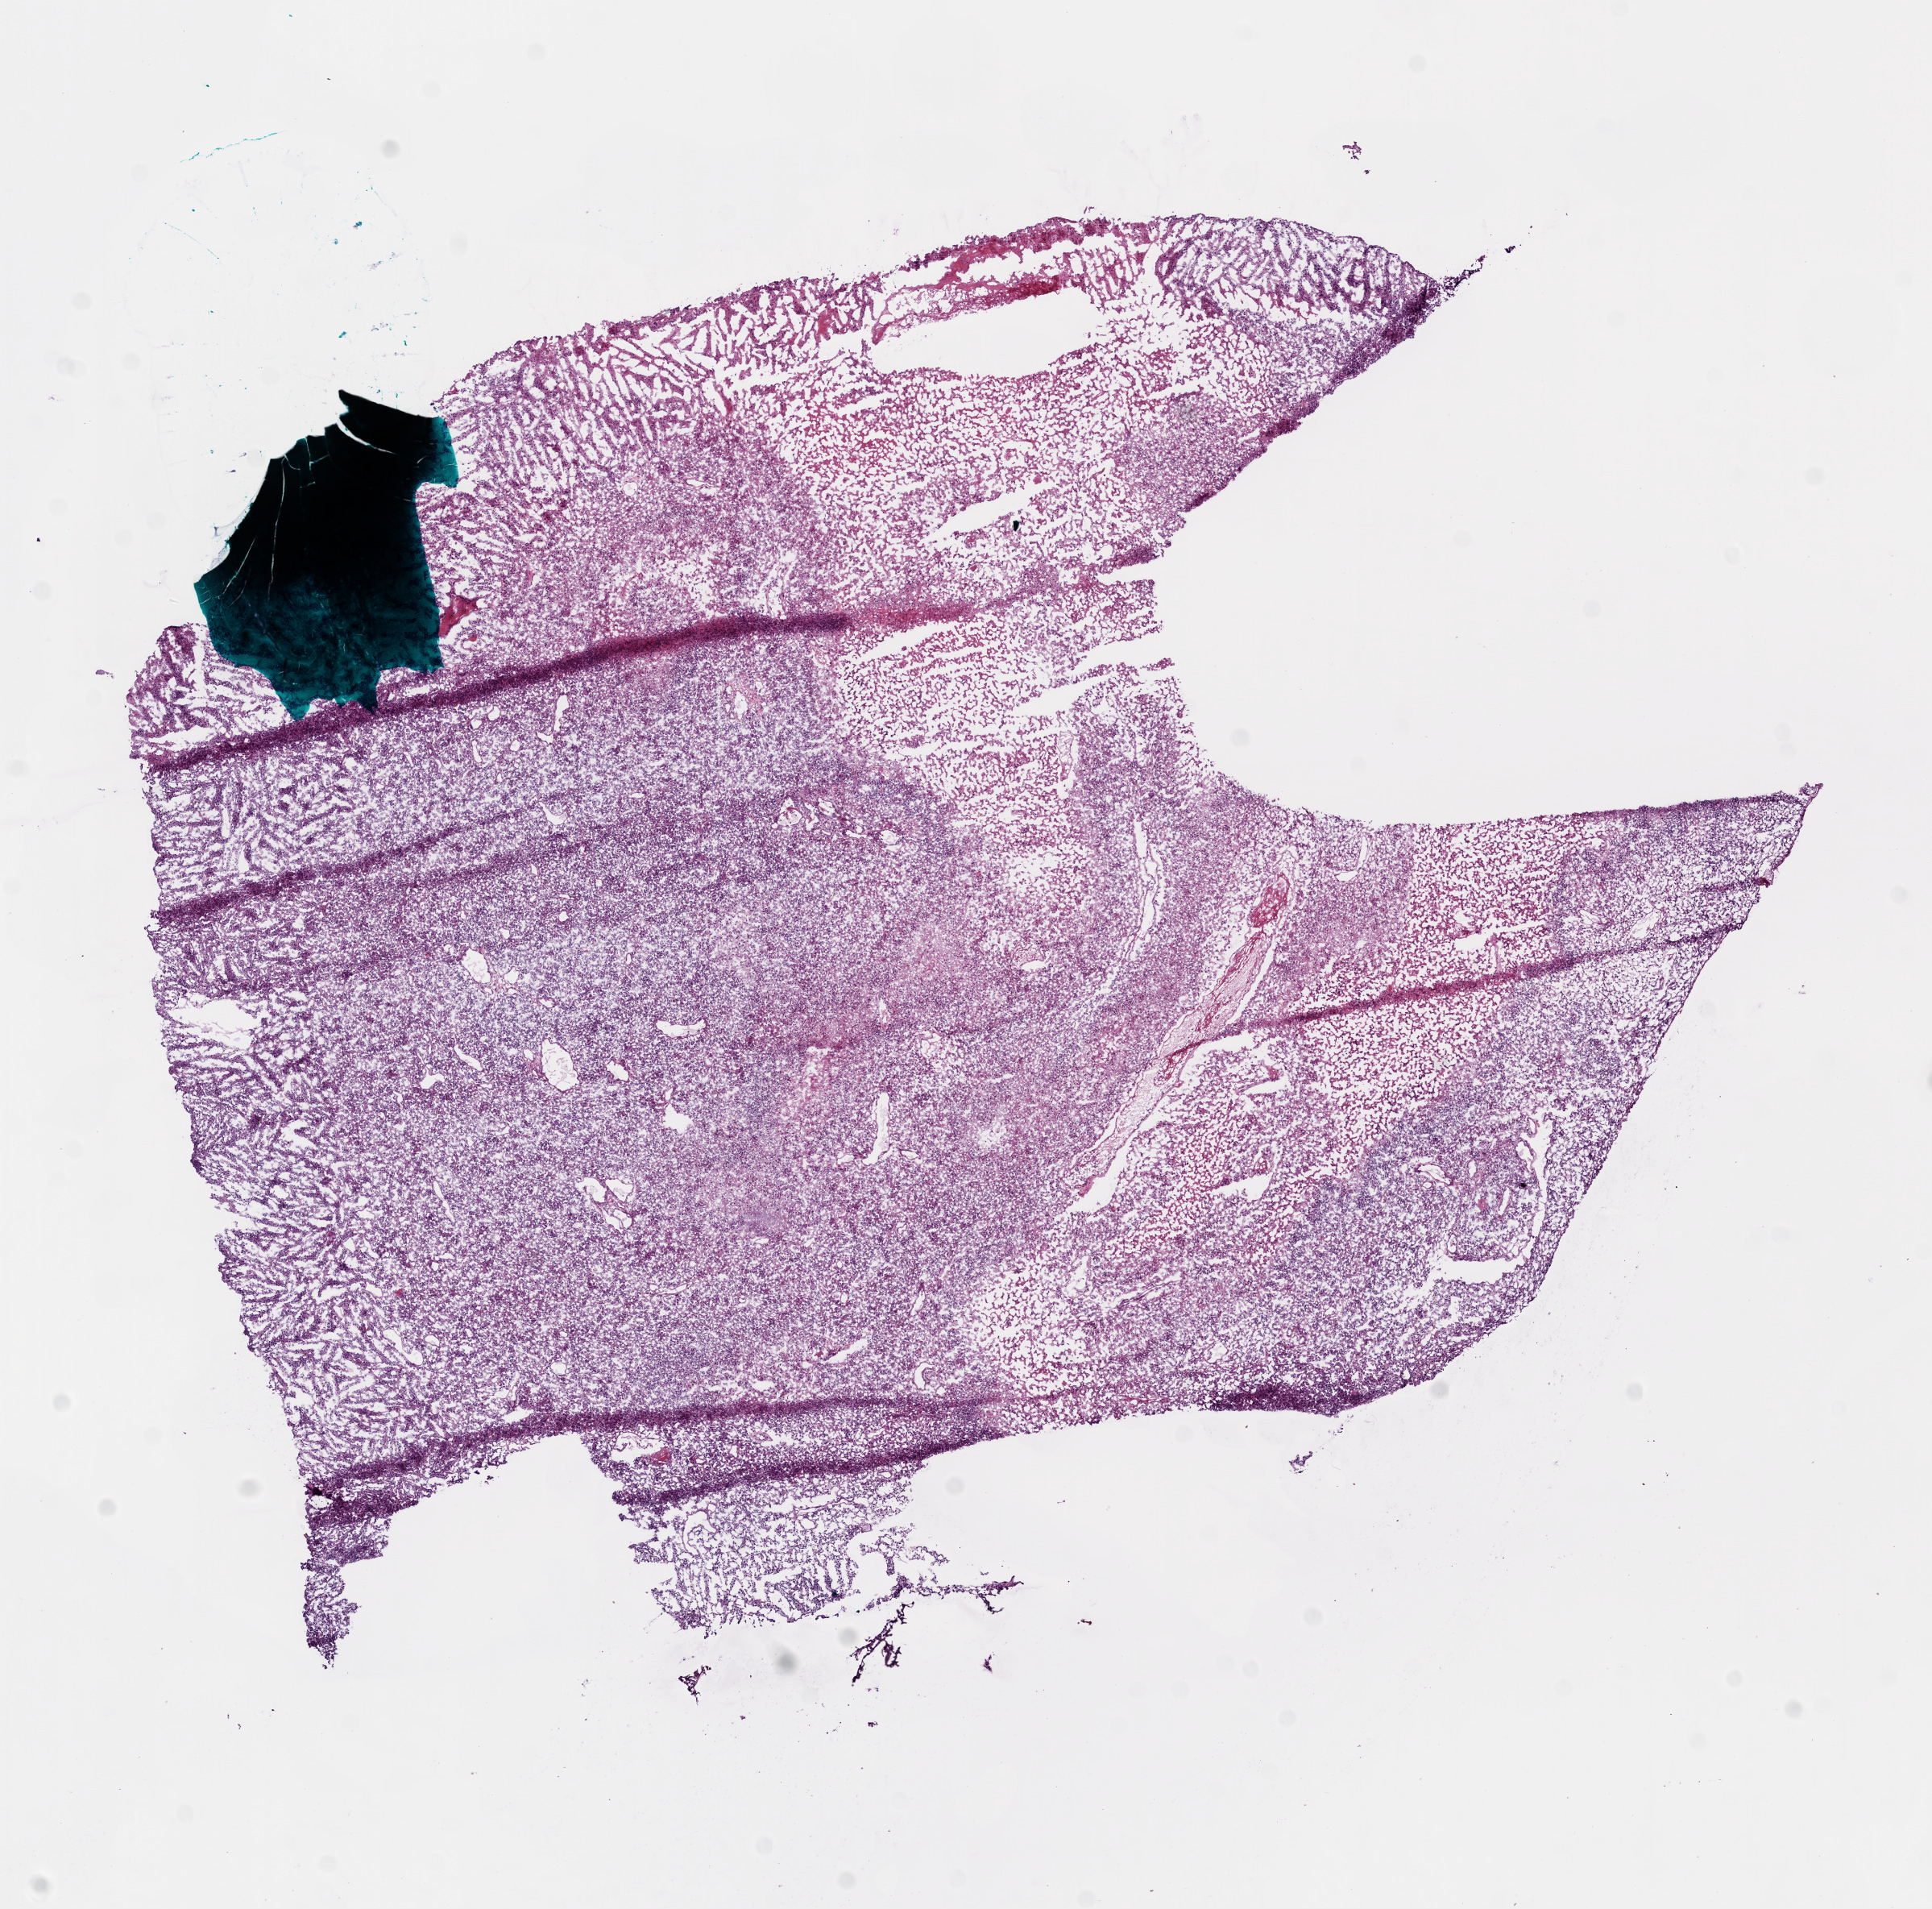
H&E-stained whole-slide image, low-resolution overview of the scanned area, about 9.7 x 9.6 mm, frozen section from the bottom of the tissue portion, sample: primary tumour, brain. Female patient; age at initial diagnosis 10 years.
Histologic diagnosis: Glioblastoma.